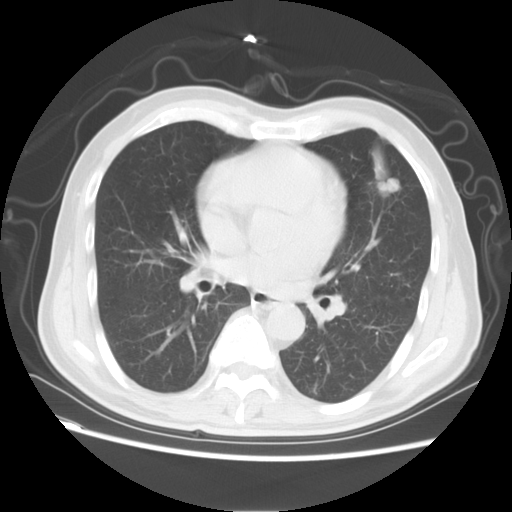
Chest CT, one axial slice. Lung window (W 1500 / L -600 HU). 5 mm slice thickness. 512 × 512 image matrix, field of view 368 × 368 mm. Male patient, age 60 years. Case-level facts recorded for this patient, not image findings: clinical TNM (as recorded): T2a N0 M0.
Outlined on this slice (bounding box drawn by a radiologist):
- lung tumour (recorded histology: adenocarcinoma): box from (x=364, y=150) to (x=406, y=209) px